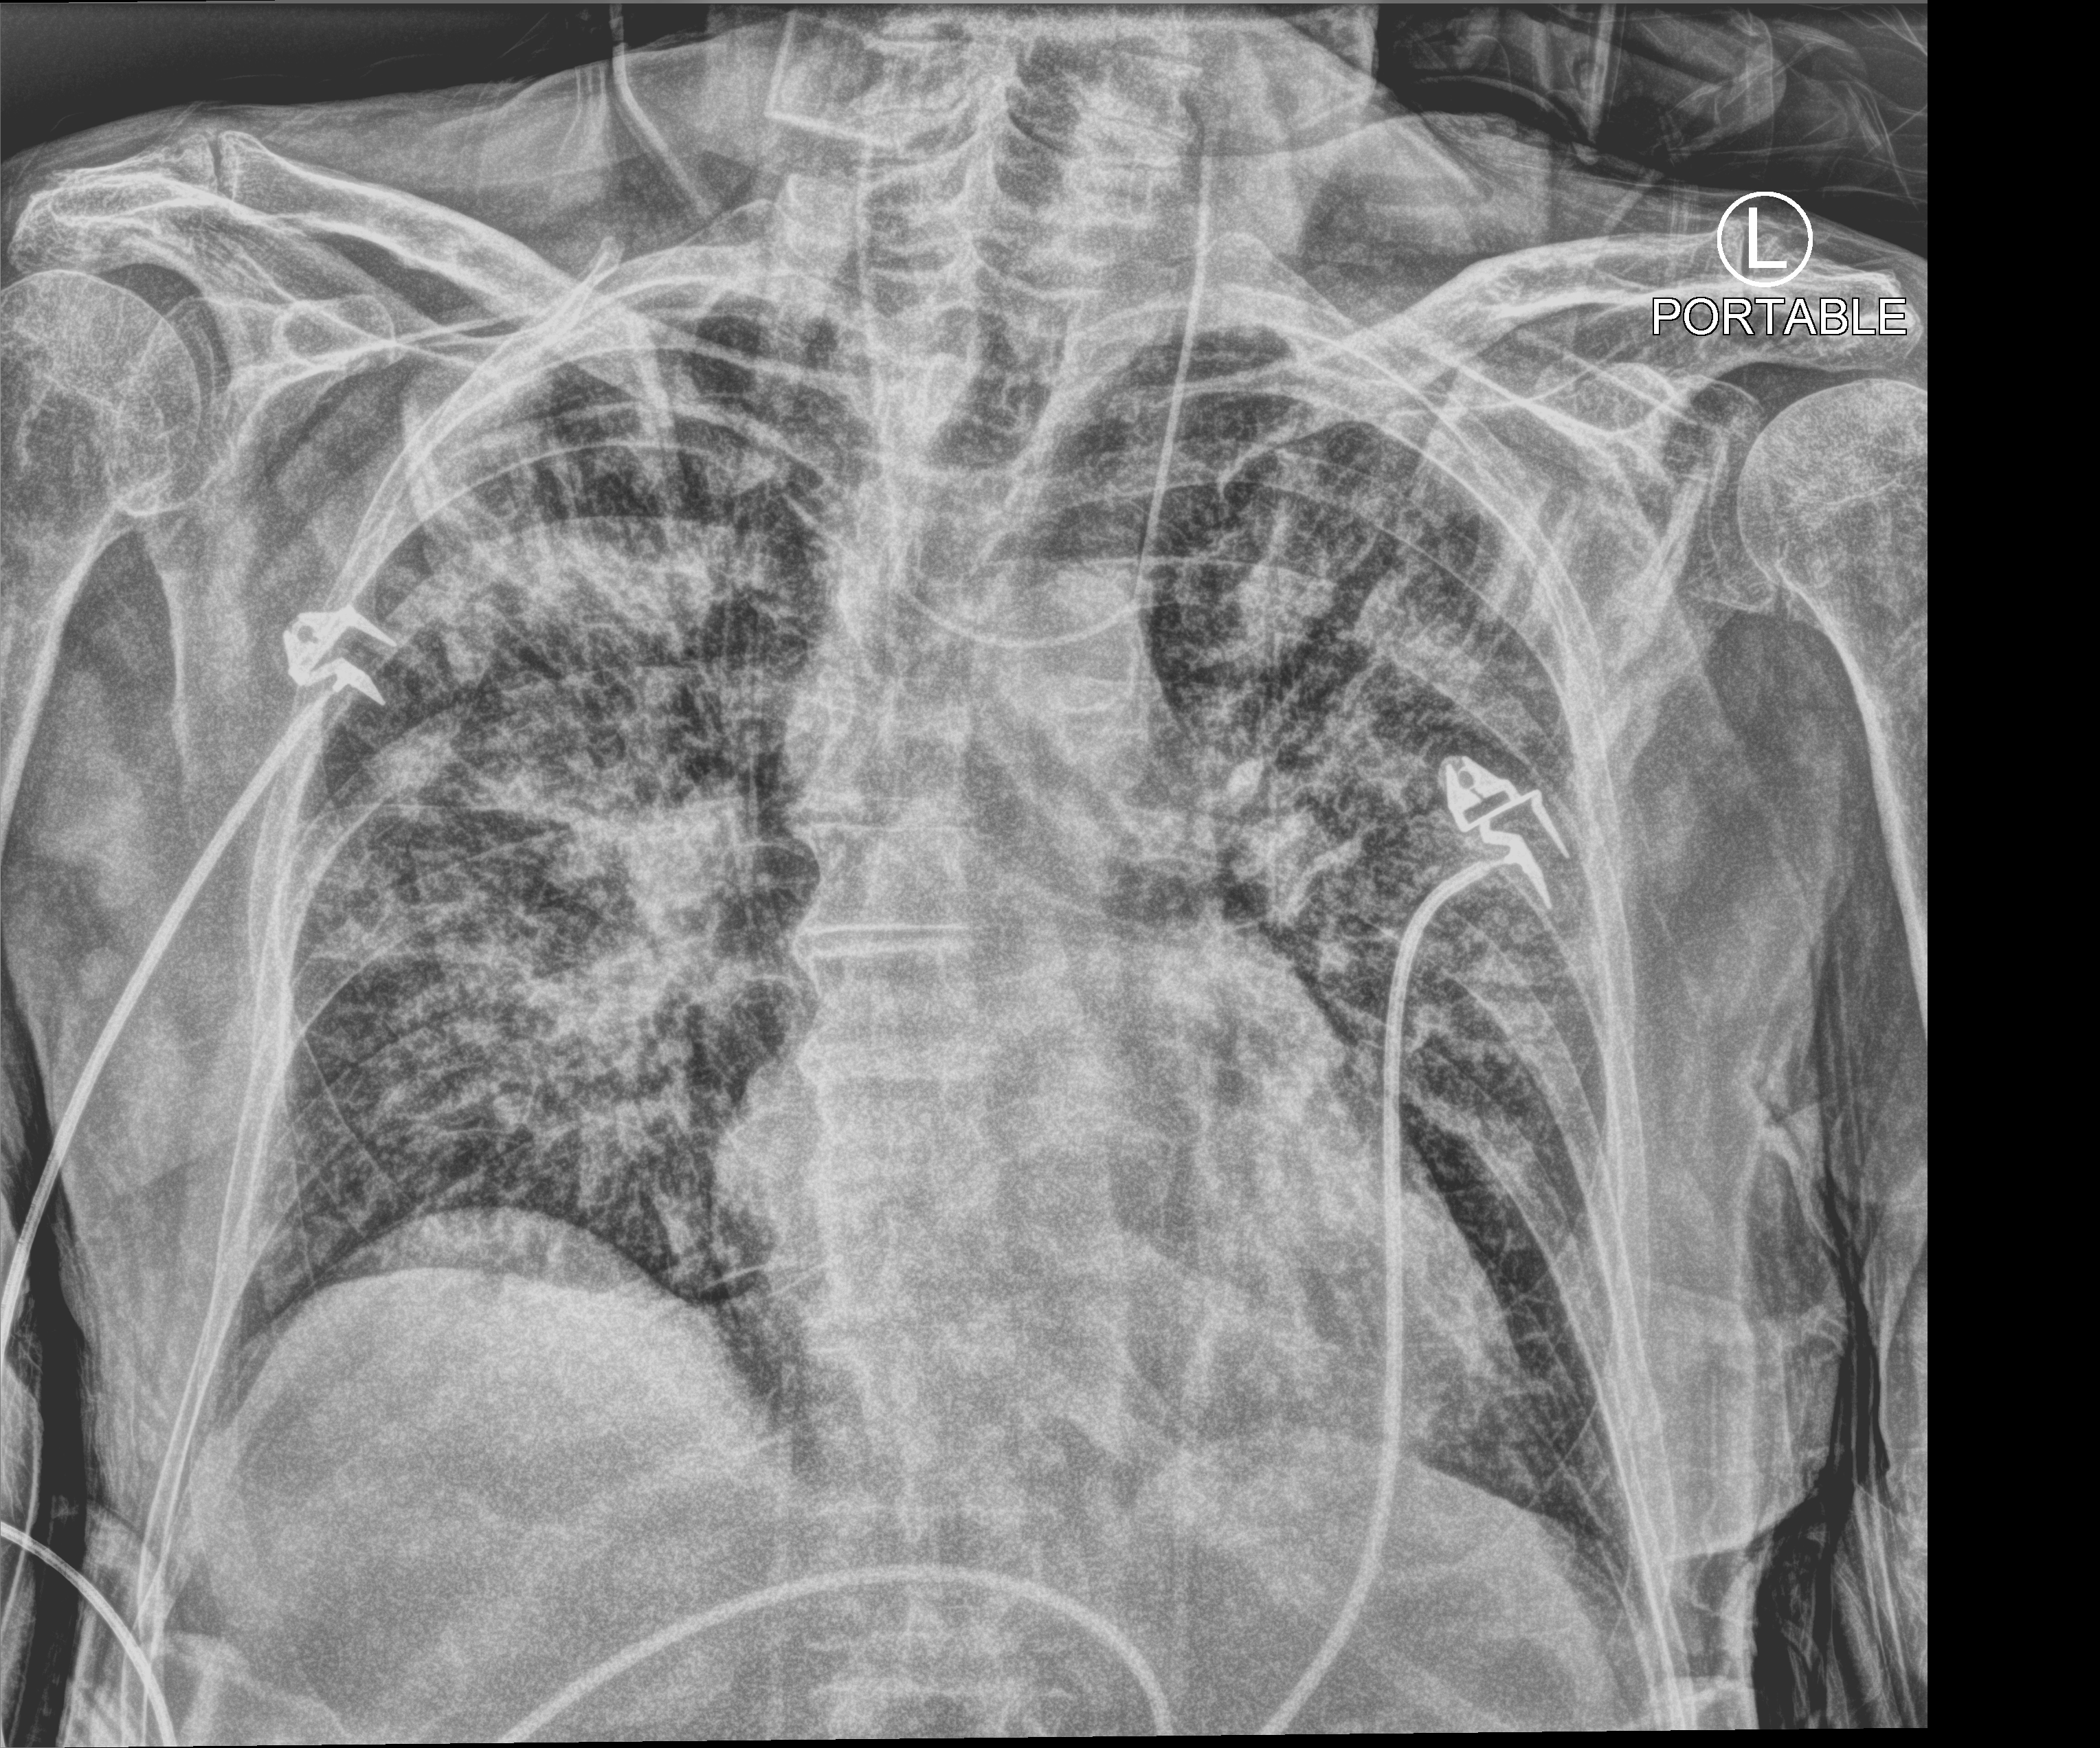
Portable chest radiograph, anteroposterior (AP) projection. Patient hospitalised with COVID-19; male, aged 75–90 years.
From the hospital-stay record, not from the radiograph (when in the stay this image was taken is not recorded):
- COPD (admission record): no